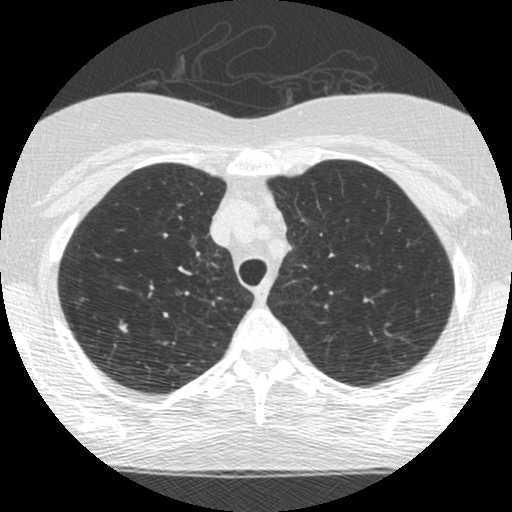
Low-dose screening chest CT, one axial slice; position 207 of 253 along the scan axis; 120 kVp; lung window (W 1500 / L -600 HU); 1.25 mm slice thickness; 512 × 512 image matrix, field of view 294 × 294 mm.
Structures marked on this image (expert manual segmentation):
- lesion 1 (tumor, upper lobe of right lung): bounding box [x1, y1, x2, y2] px = [119, 324, 128, 332]